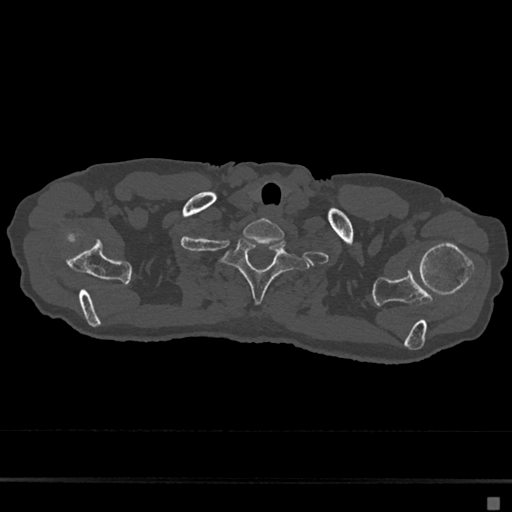
CT including the spine, one axial slice; position 611 of 797 along the scan axis; reconstruction kernel Br40s/3; 120 kVp; bone window (W 1800 / L 400 HU); 0.5 mm slice thickness; 512 × 512 image matrix, field of view 360 × 360 mm. Patient: female, 68 years. Case-level facts recorded for this patient, not image findings: primary cancer: renal.
Outlined on this slice (semi-automatically segmented with operator editing):
- T1 vertebra: box from (x=222, y=237) to (x=309, y=303) px